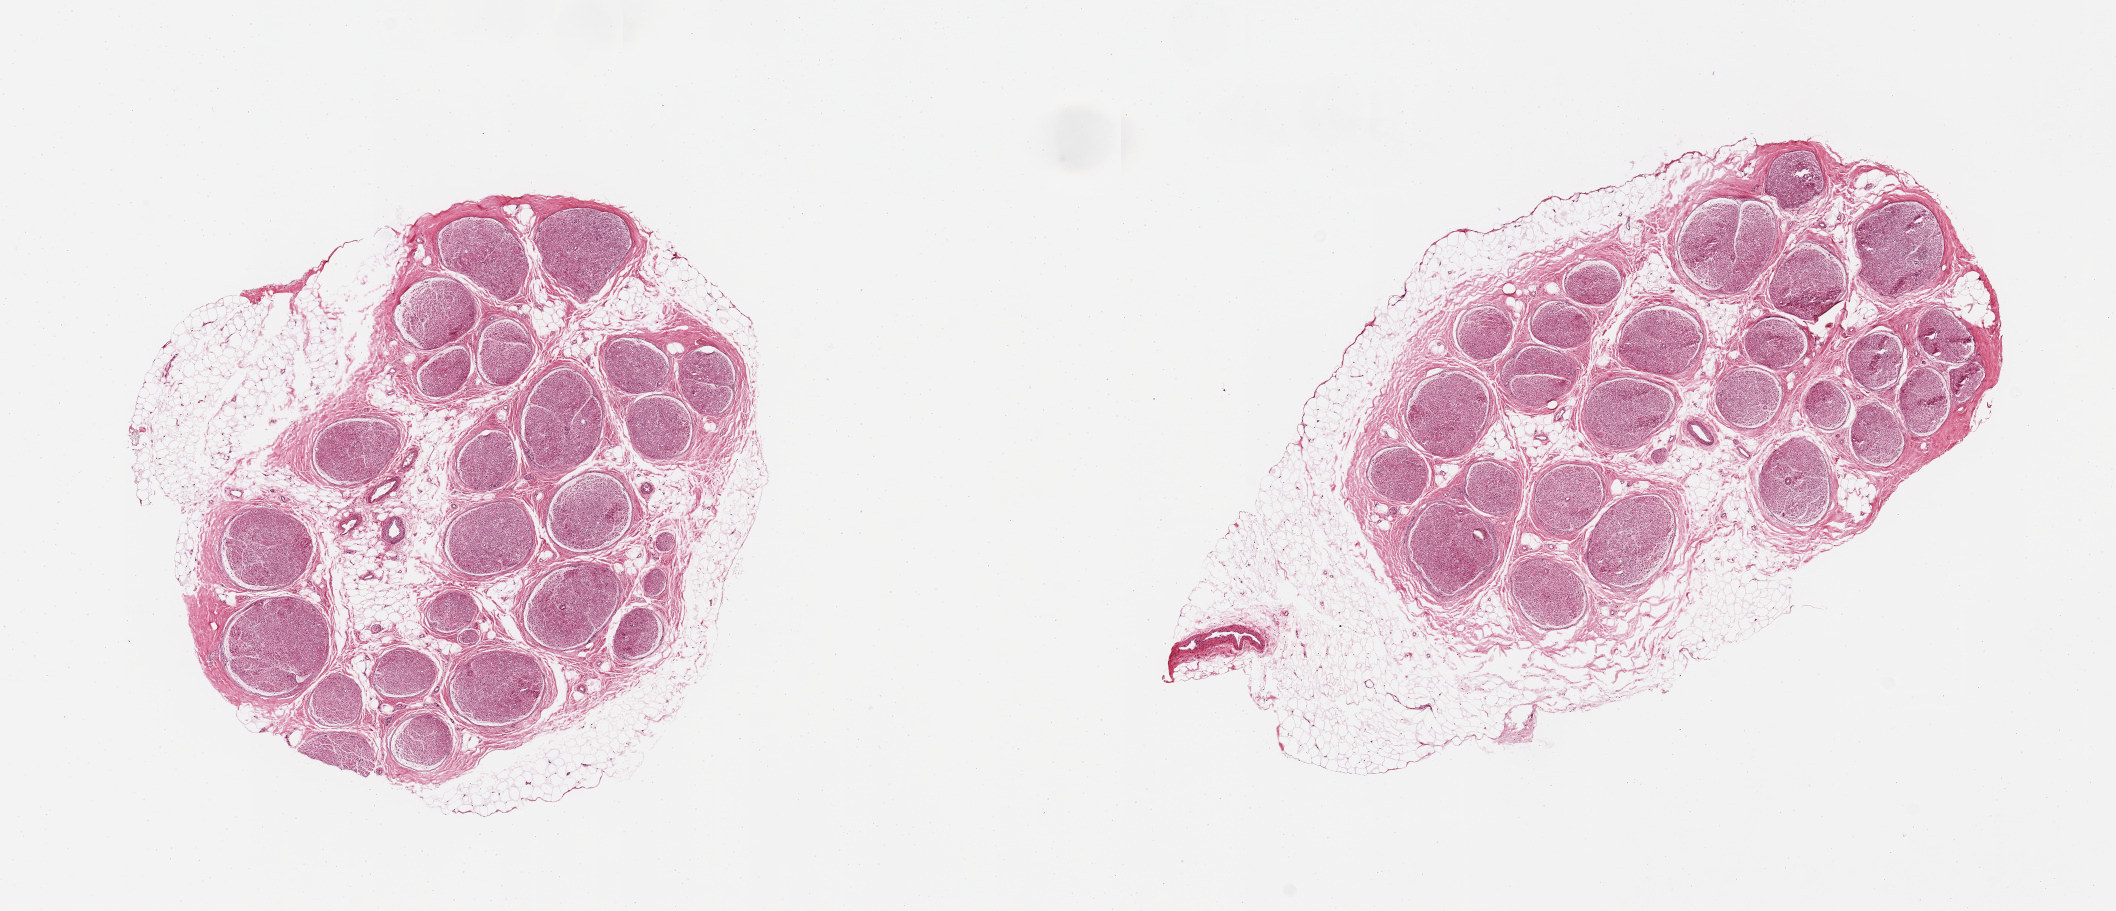
H&E whole-slide image, shown as a low-resolution overview of the whole scanned area (about 16.7 x 7.2 mm, acquisition: 20x scan); PAXgene-fixed, paraffin-embedded tissue; section of tibial nerve (target tissue); donor tissue sample. Donor sex: male.
Pathologist's review note for this sample: 2 pieces, rims of adherent fat, 1-1.5mm.